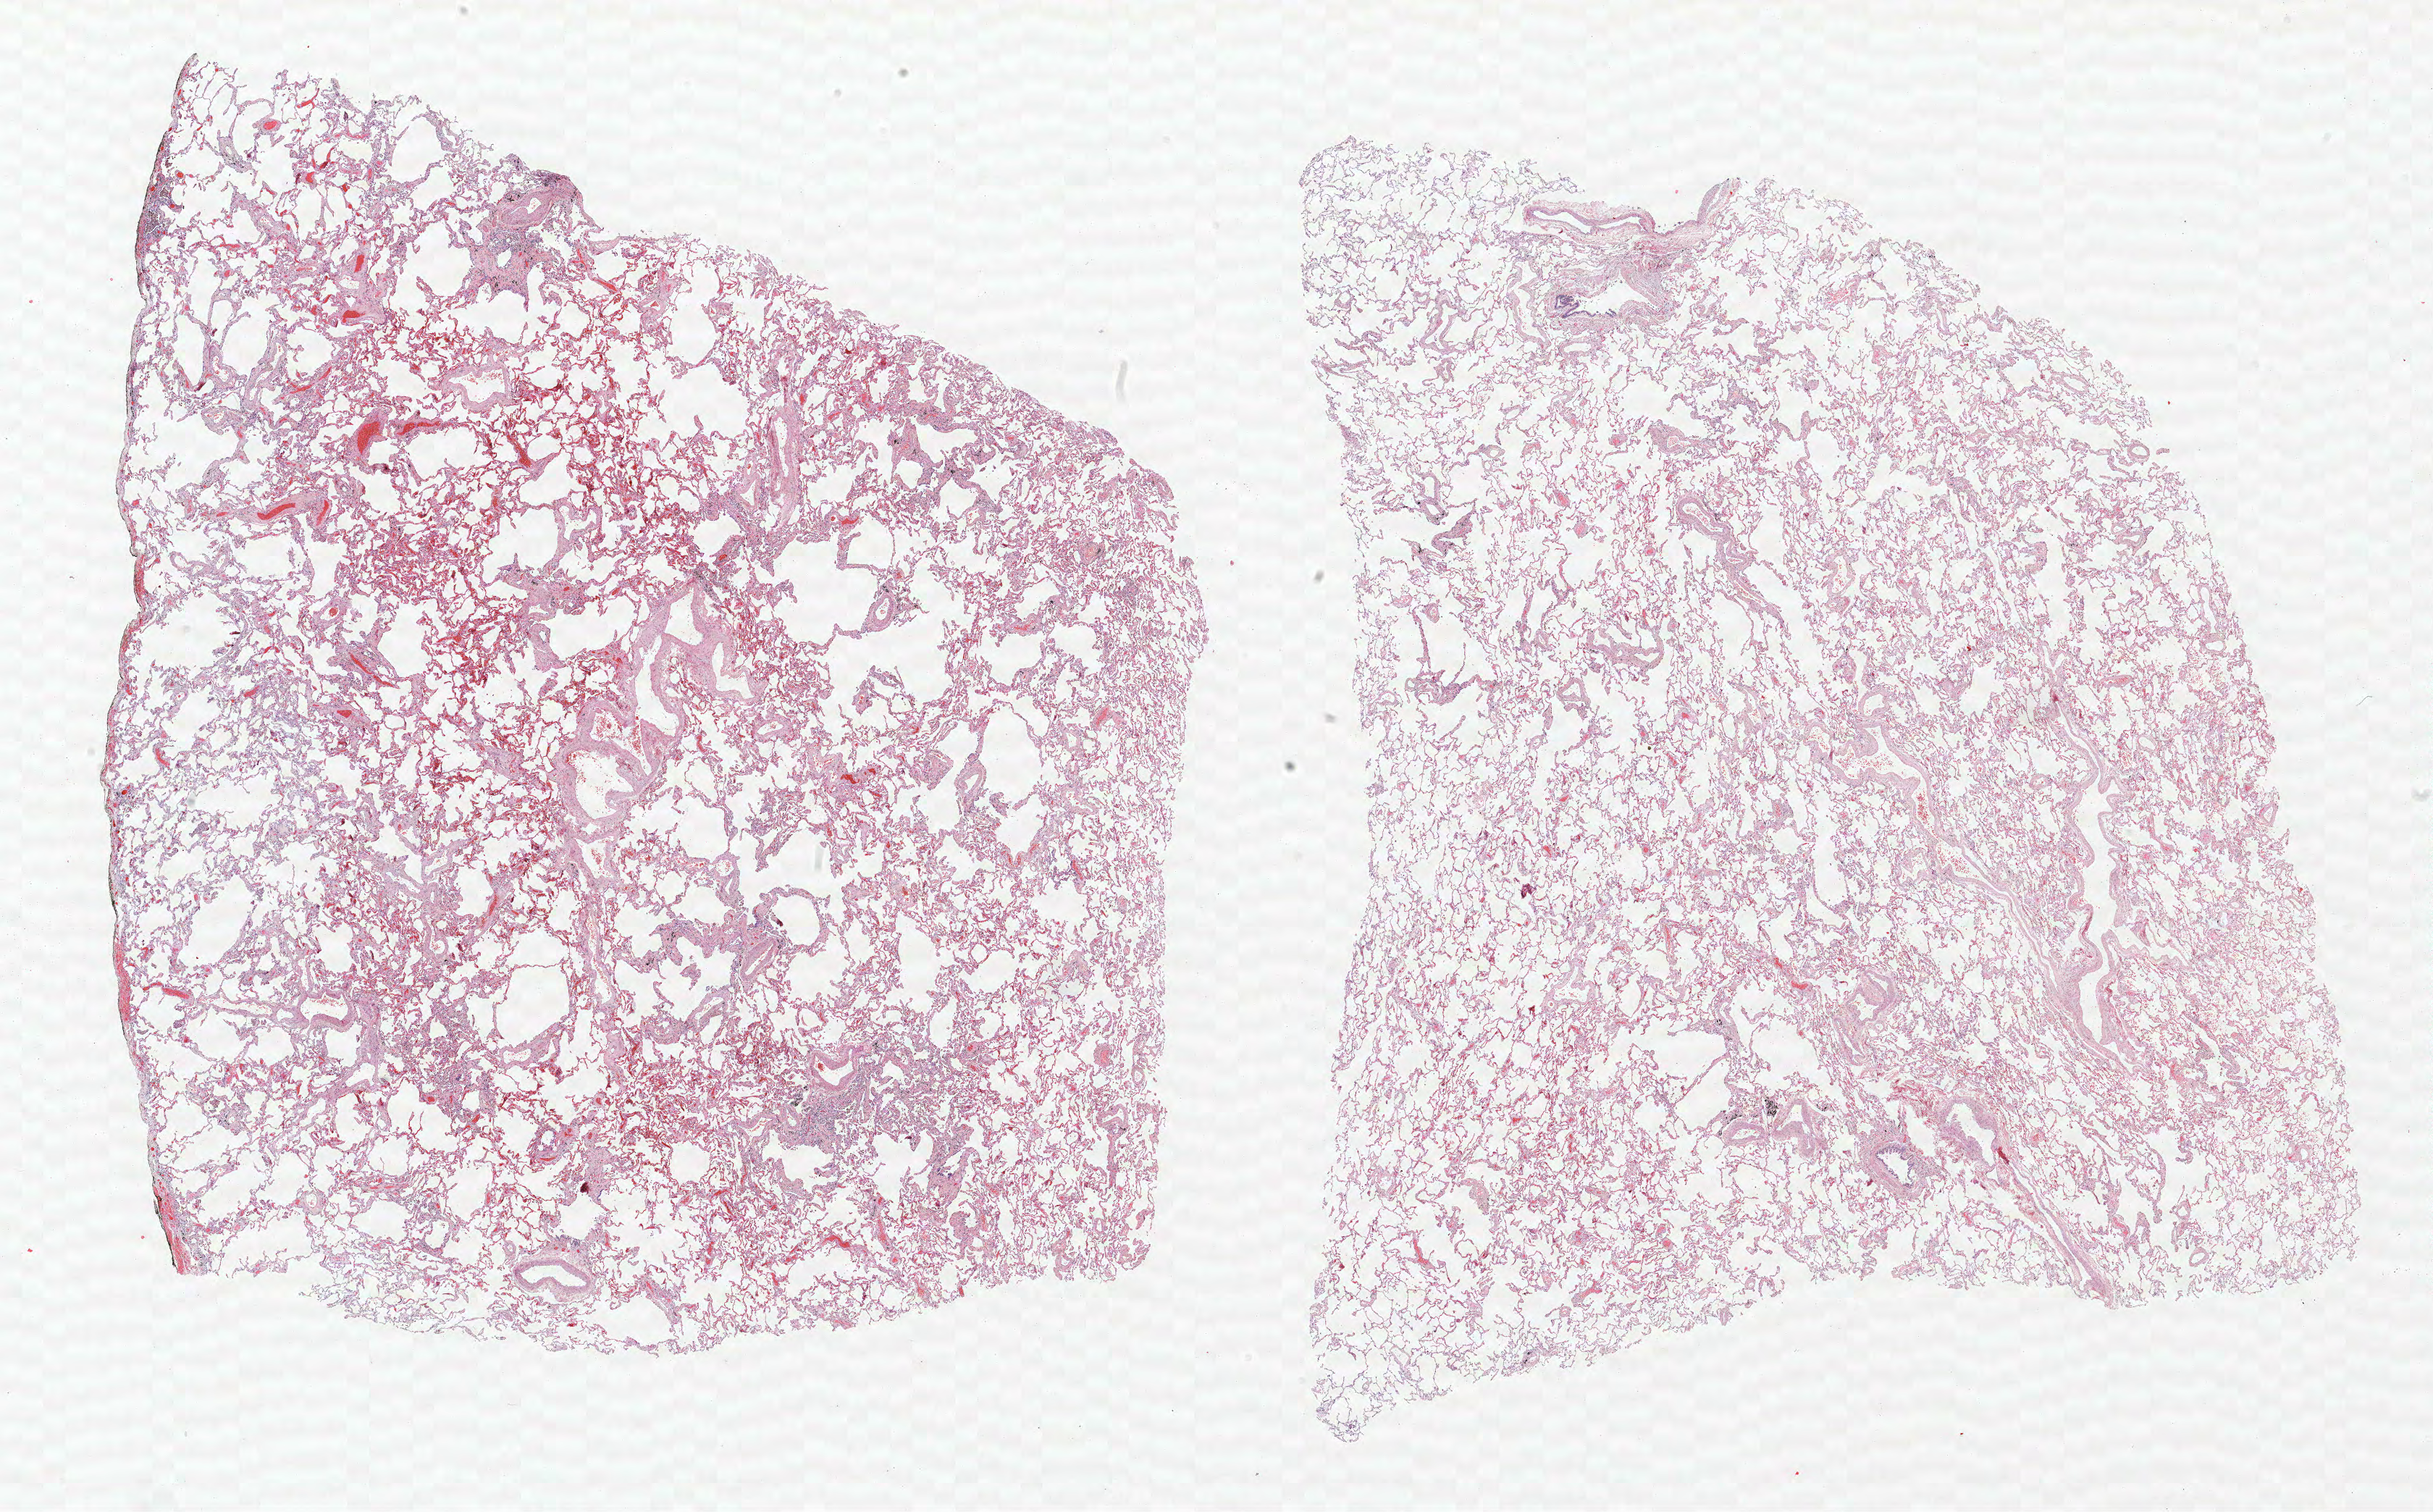
Whole-slide histology image, Hematoxylin and eosin (H&E) stained — whole scanned area (about 26.9 x 16.7 mm) shown as a low-resolution overview; FFPE section; lung. Male, age 70 at enrolment. Current smoker at enrolment. Grade: poorly differentiated (G3).
ICD-O-3 topography: upper lobe of lung (C34.1). Tumour size (pathology): 15 mm. Primary tumour location (clinical record): right upper lobe. Stage (AJCC 6th edition): IA. Participant's lung-cancer diagnosis: Large cell neuroendocrine carcinoma (ICD-O-3 8013/3).